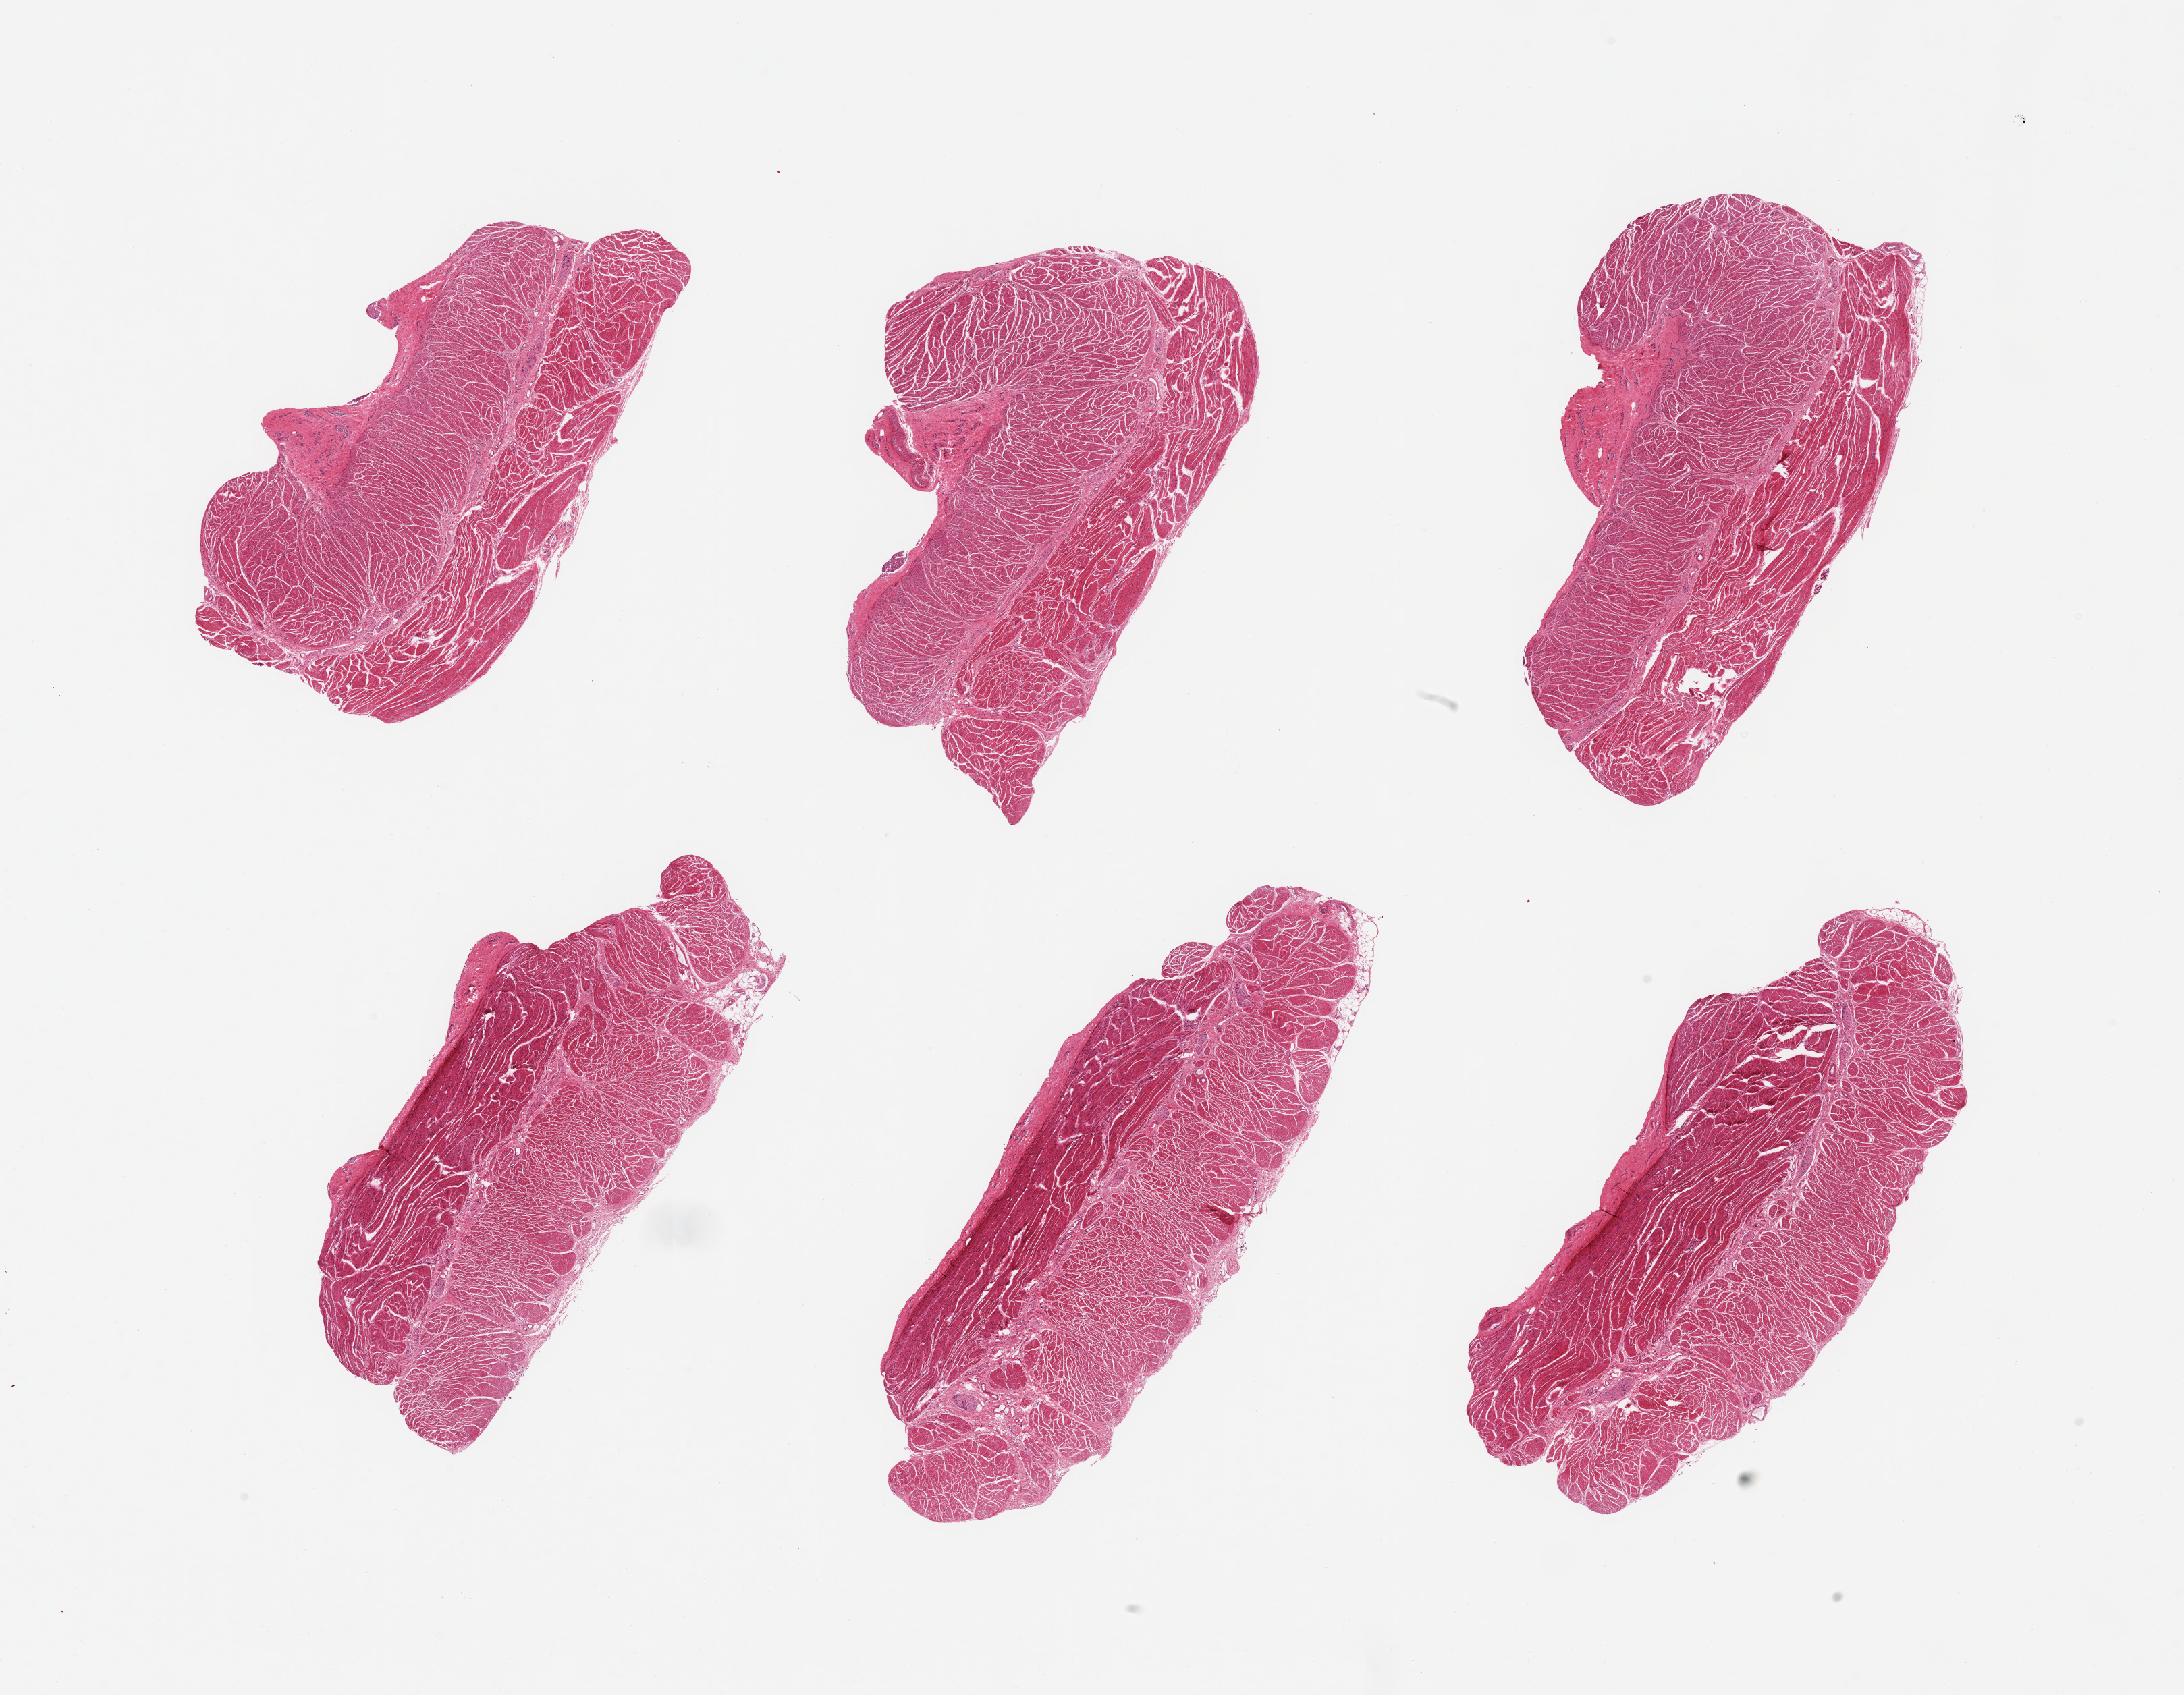
Digitized hematoxylin and eosin (H&E)-stained section, whole scanned area (about 25.6 x 19.9 mm) shown as a low-resolution overview. PAXgene-fixed paraffin-embedded (PFPE) section. Section of gastroesophageal junction (target tissue). Tissue donor sample. Donor: male.
Review note (as recorded): 6 pieces, confirmed target muscularis.